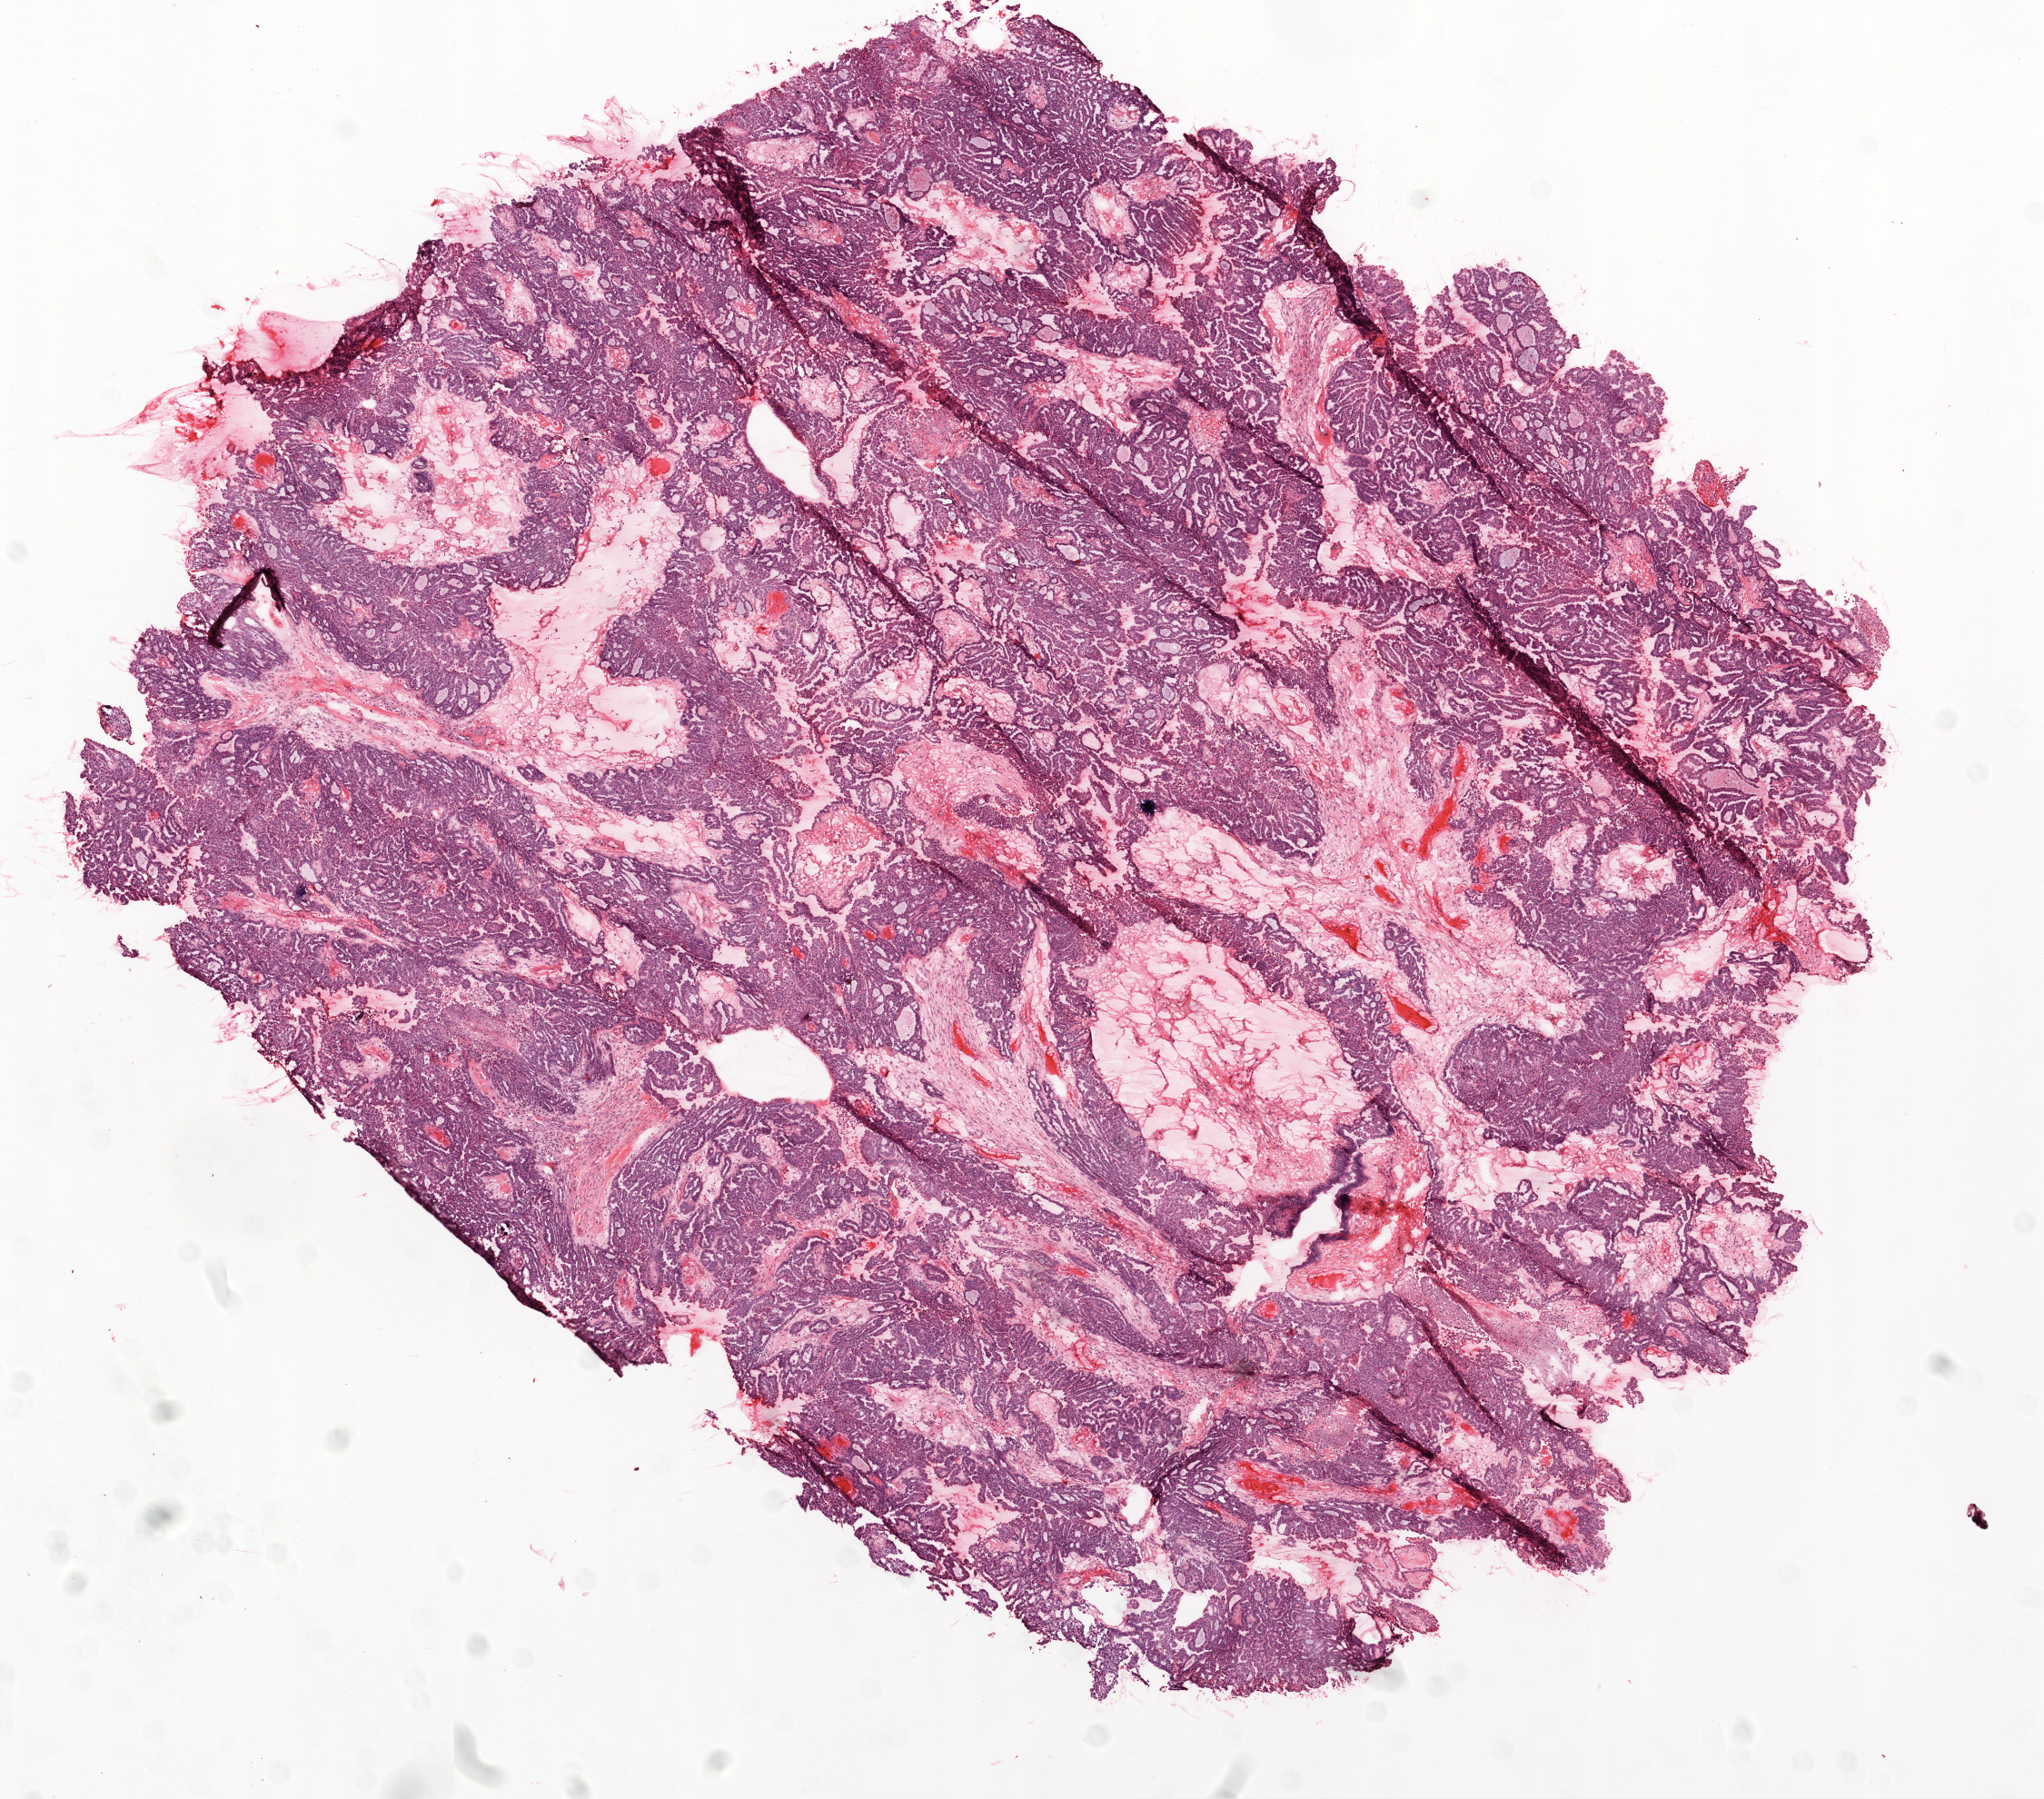
H&E whole-slide image — whole scanned area (about 9.0 x 7.9 mm) shown as a low-resolution overview; frozen section from the top of the tissue portion; ovary, primary tumour sample. Female patient; age at initial diagnosis 64 years. Histologic grade: G1 (well differentiated). Pathologist review of this section (percent, as recorded): tumour cells 95%, tumour nuclei 95%, normal cells 0%, stromal cells 5%, necrosis 0%.
Histologic diagnosis: Serous cystadenocarcinoma, NOS. Laterality: bilateral. FIGO stage: IIIC.